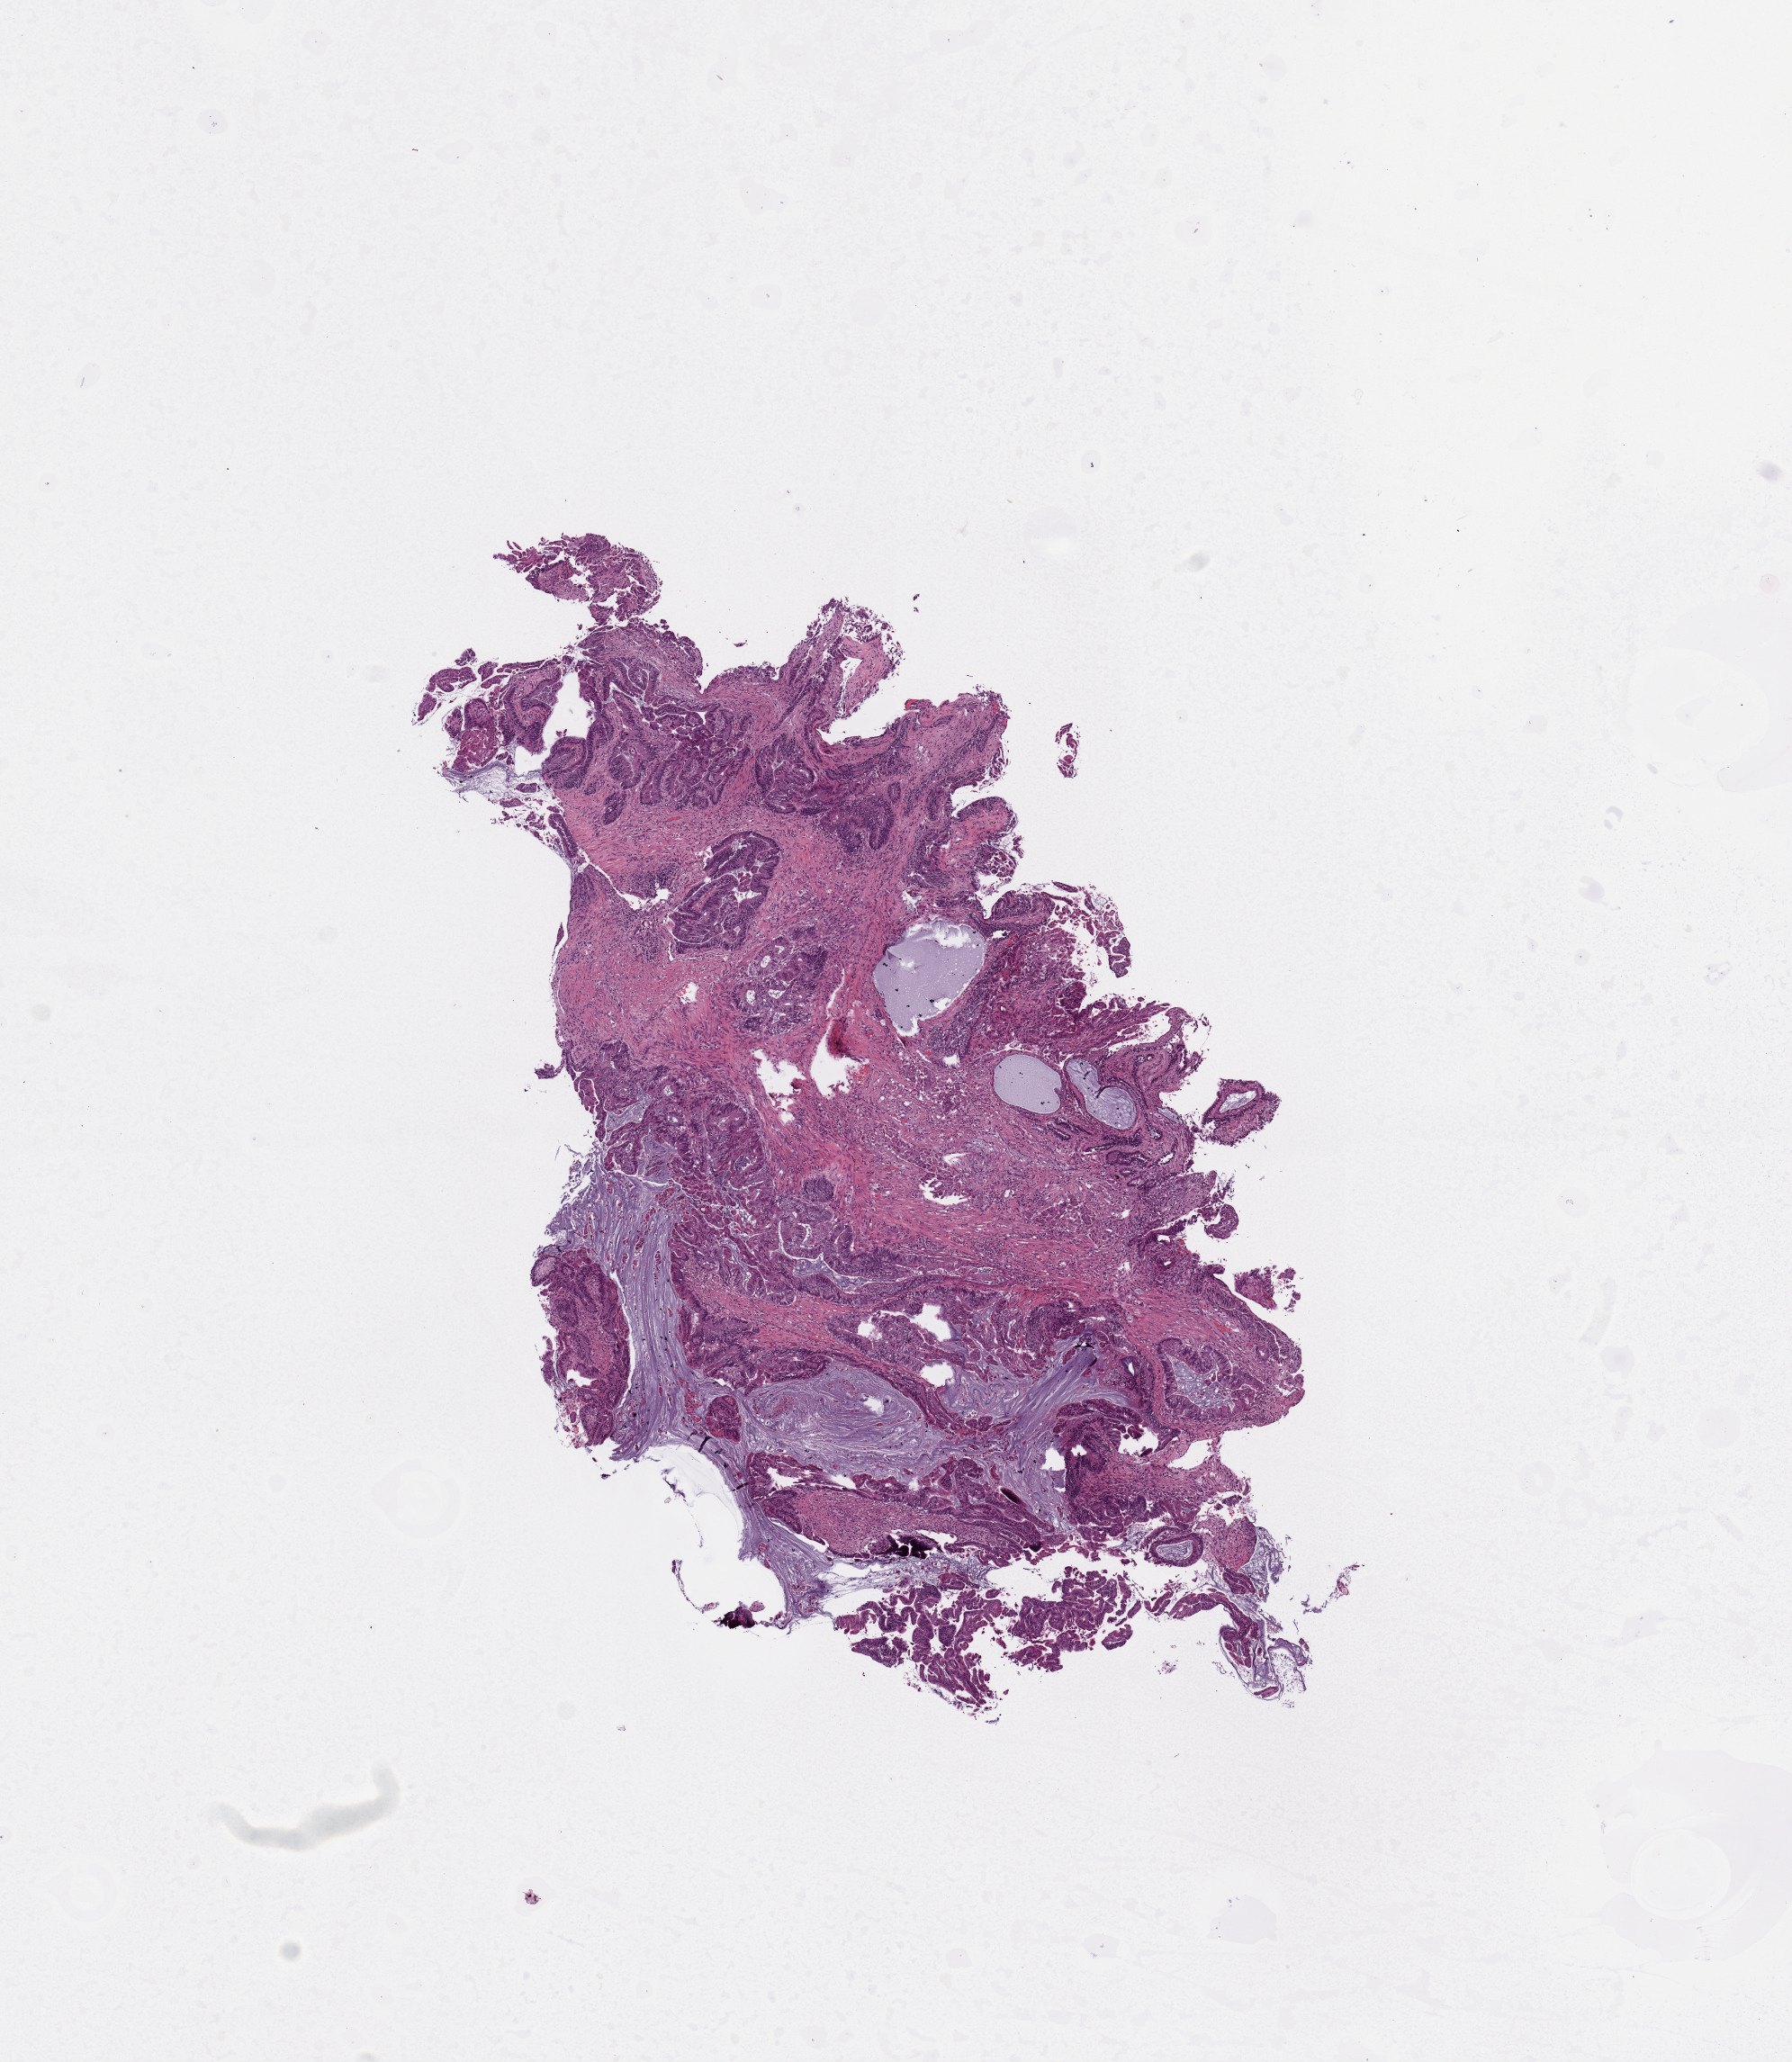
H&E whole-slide image, shown as a low-resolution overview of the whole scanned area (about 7.9 x 9.1 mm, slide scanned at 20x), tumour tissue sample, uterus. Patient: female, age 46 years. Histologic grade: G2 (moderately differentiated).
- AJCC pathologic stage: I
- diagnosis: Endometrioid adenocarcinoma, NOS